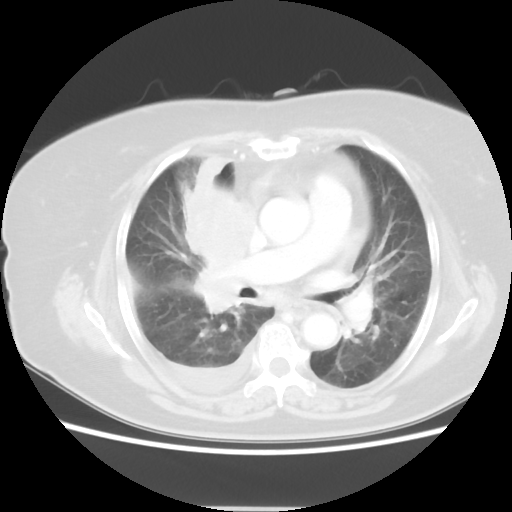
Chest CT, one axial slice; slice 28 of 48 in the series (ordered by position); reconstruction kernel STANDARD; 120 kVp; lung window (W 1500 / L -600 HU); 5 mm slice thickness; 512 × 512 image matrix, field of view 360 × 360 mm. Female patient, age 73 years. Case-level facts recorded for this patient, not image findings: clinical TNM (as recorded): T3 N3 M1b; histopathological grade: G3.
Structures marked on this image (rectangle marked by the reading radiologist):
- lung tumour (recorded histology: small cell carcinoma): box from (x=176, y=142) to (x=246, y=307) px